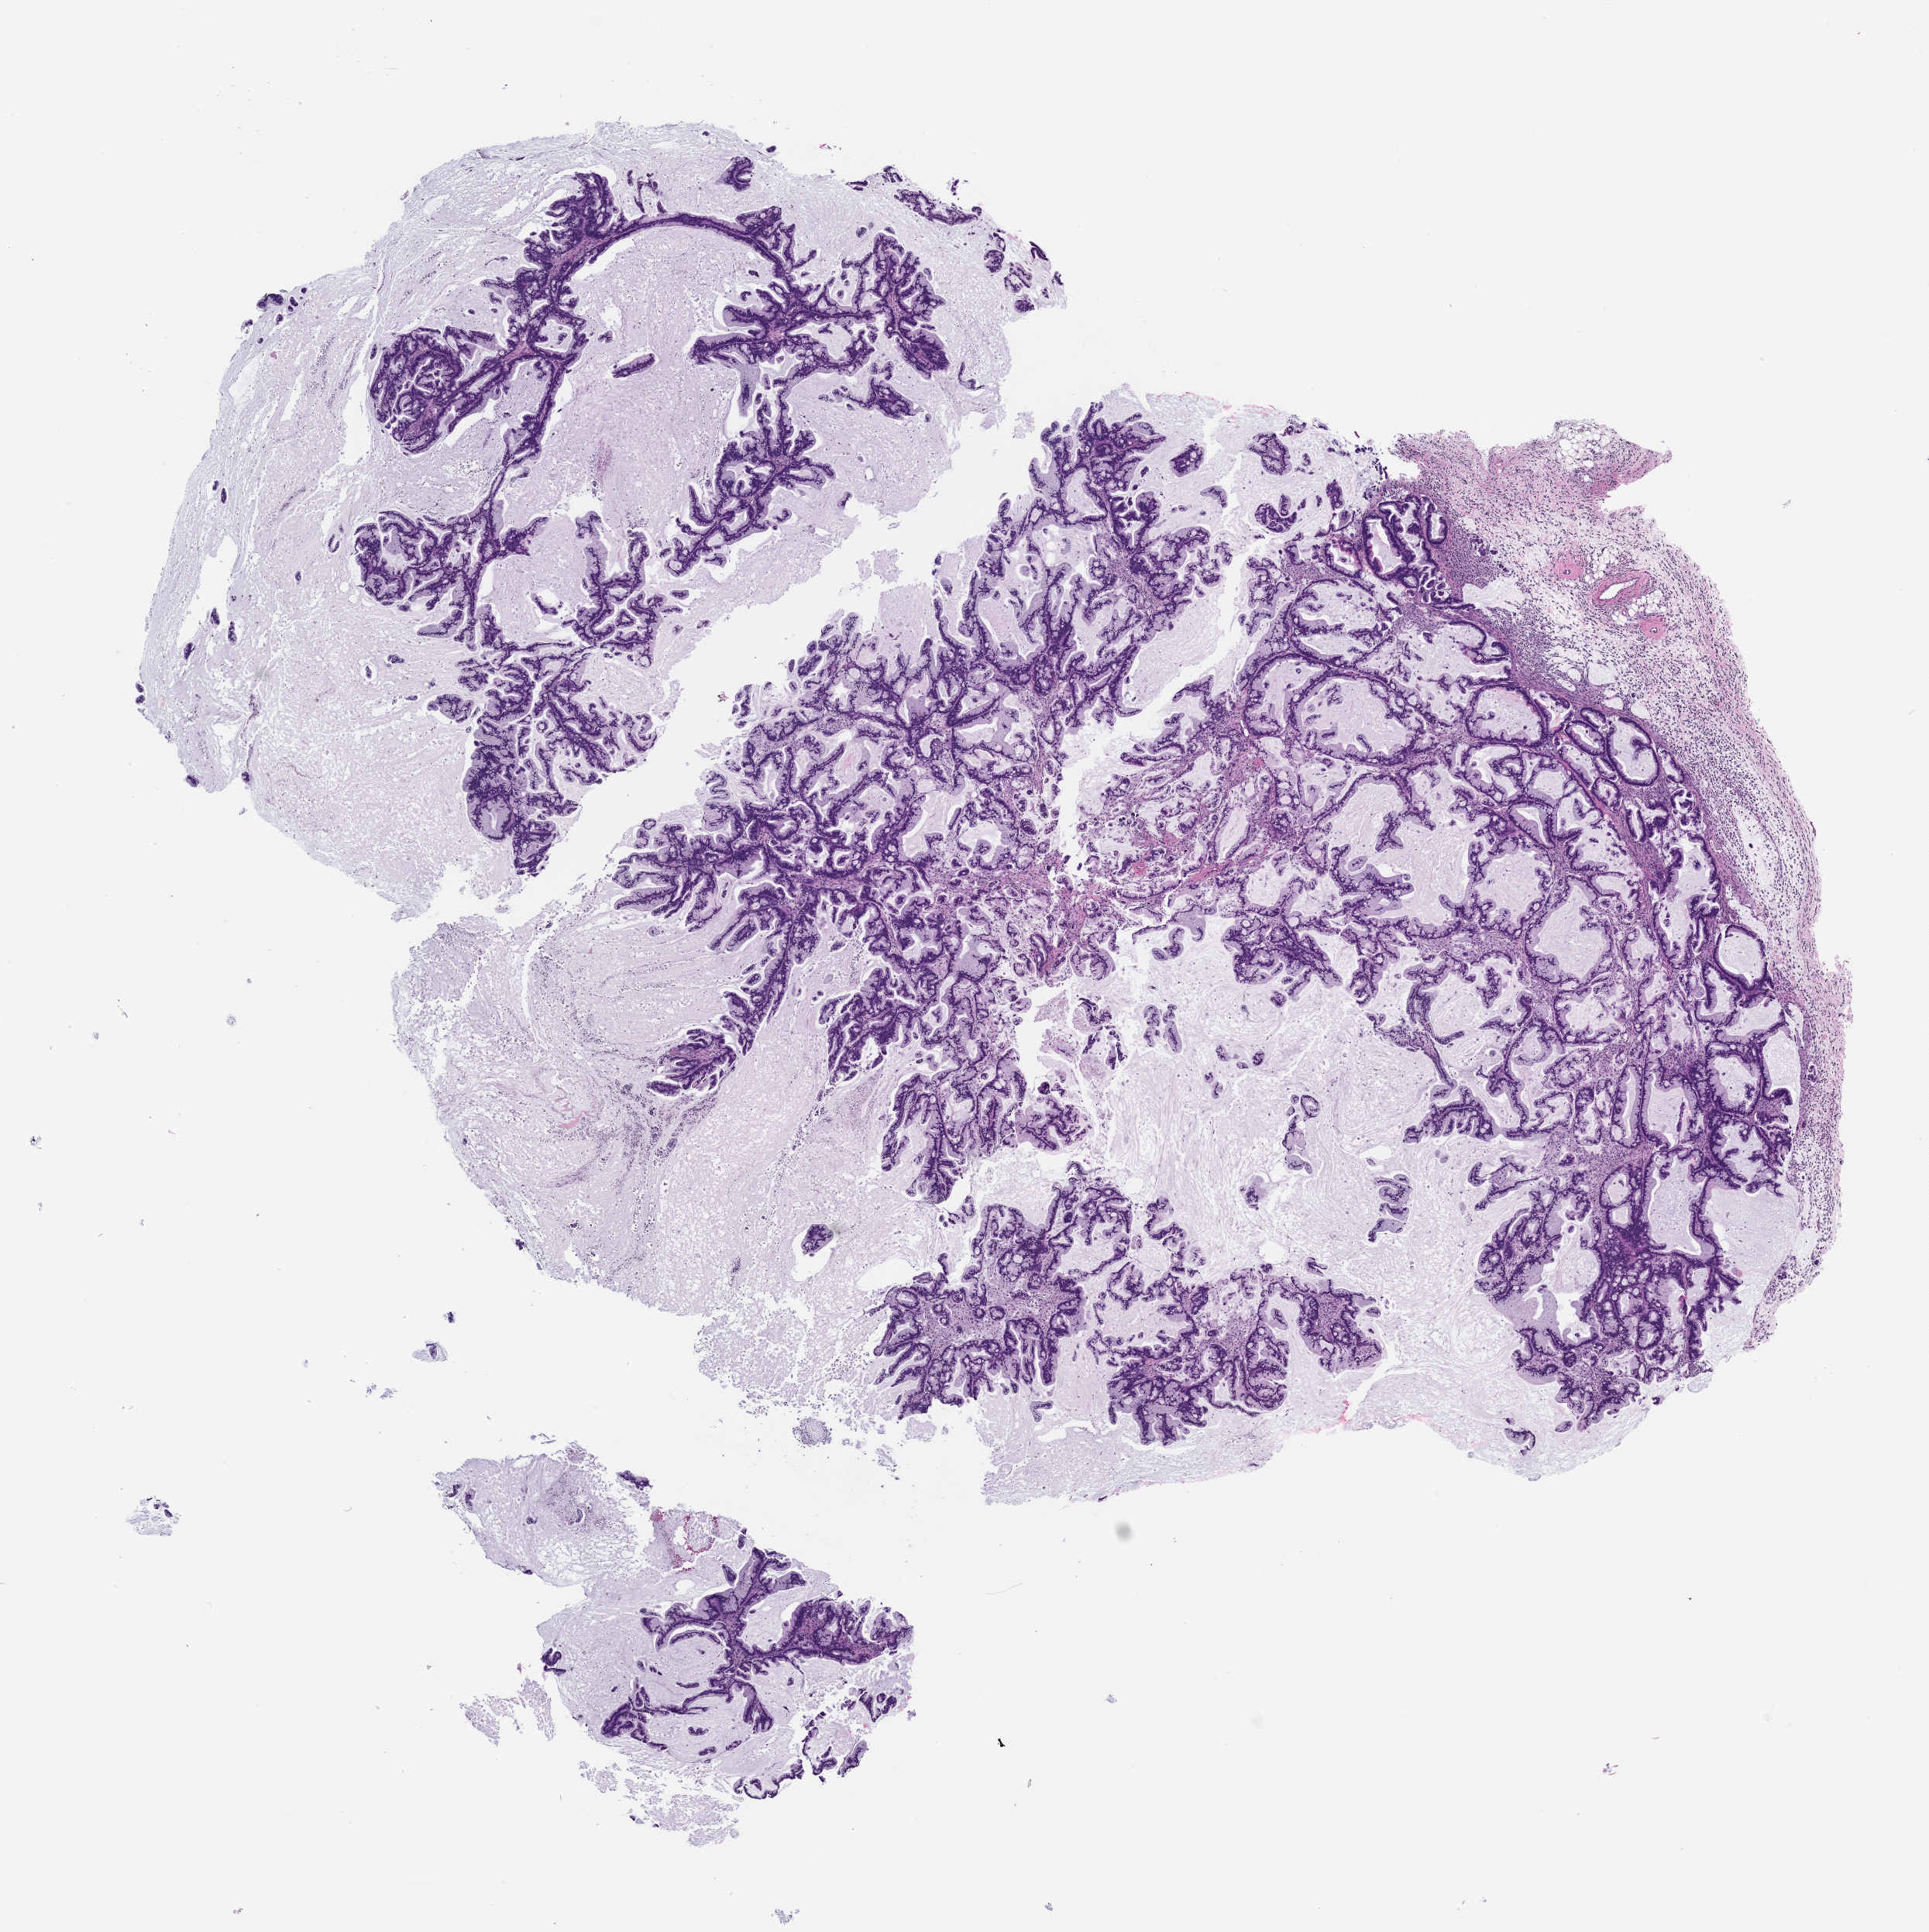
Whole-slide image, H&E: patient-derived xenograft (human tumor grown in a mouse), passage 2, a low-resolution overview of the entire scanned area, about 10.0 x 10.0 mm, formalin-fixed paraffin-embedded section, tumor site category: pancreas.
Originating patient diagnosis: Pancreatic Adenocarcinoma.